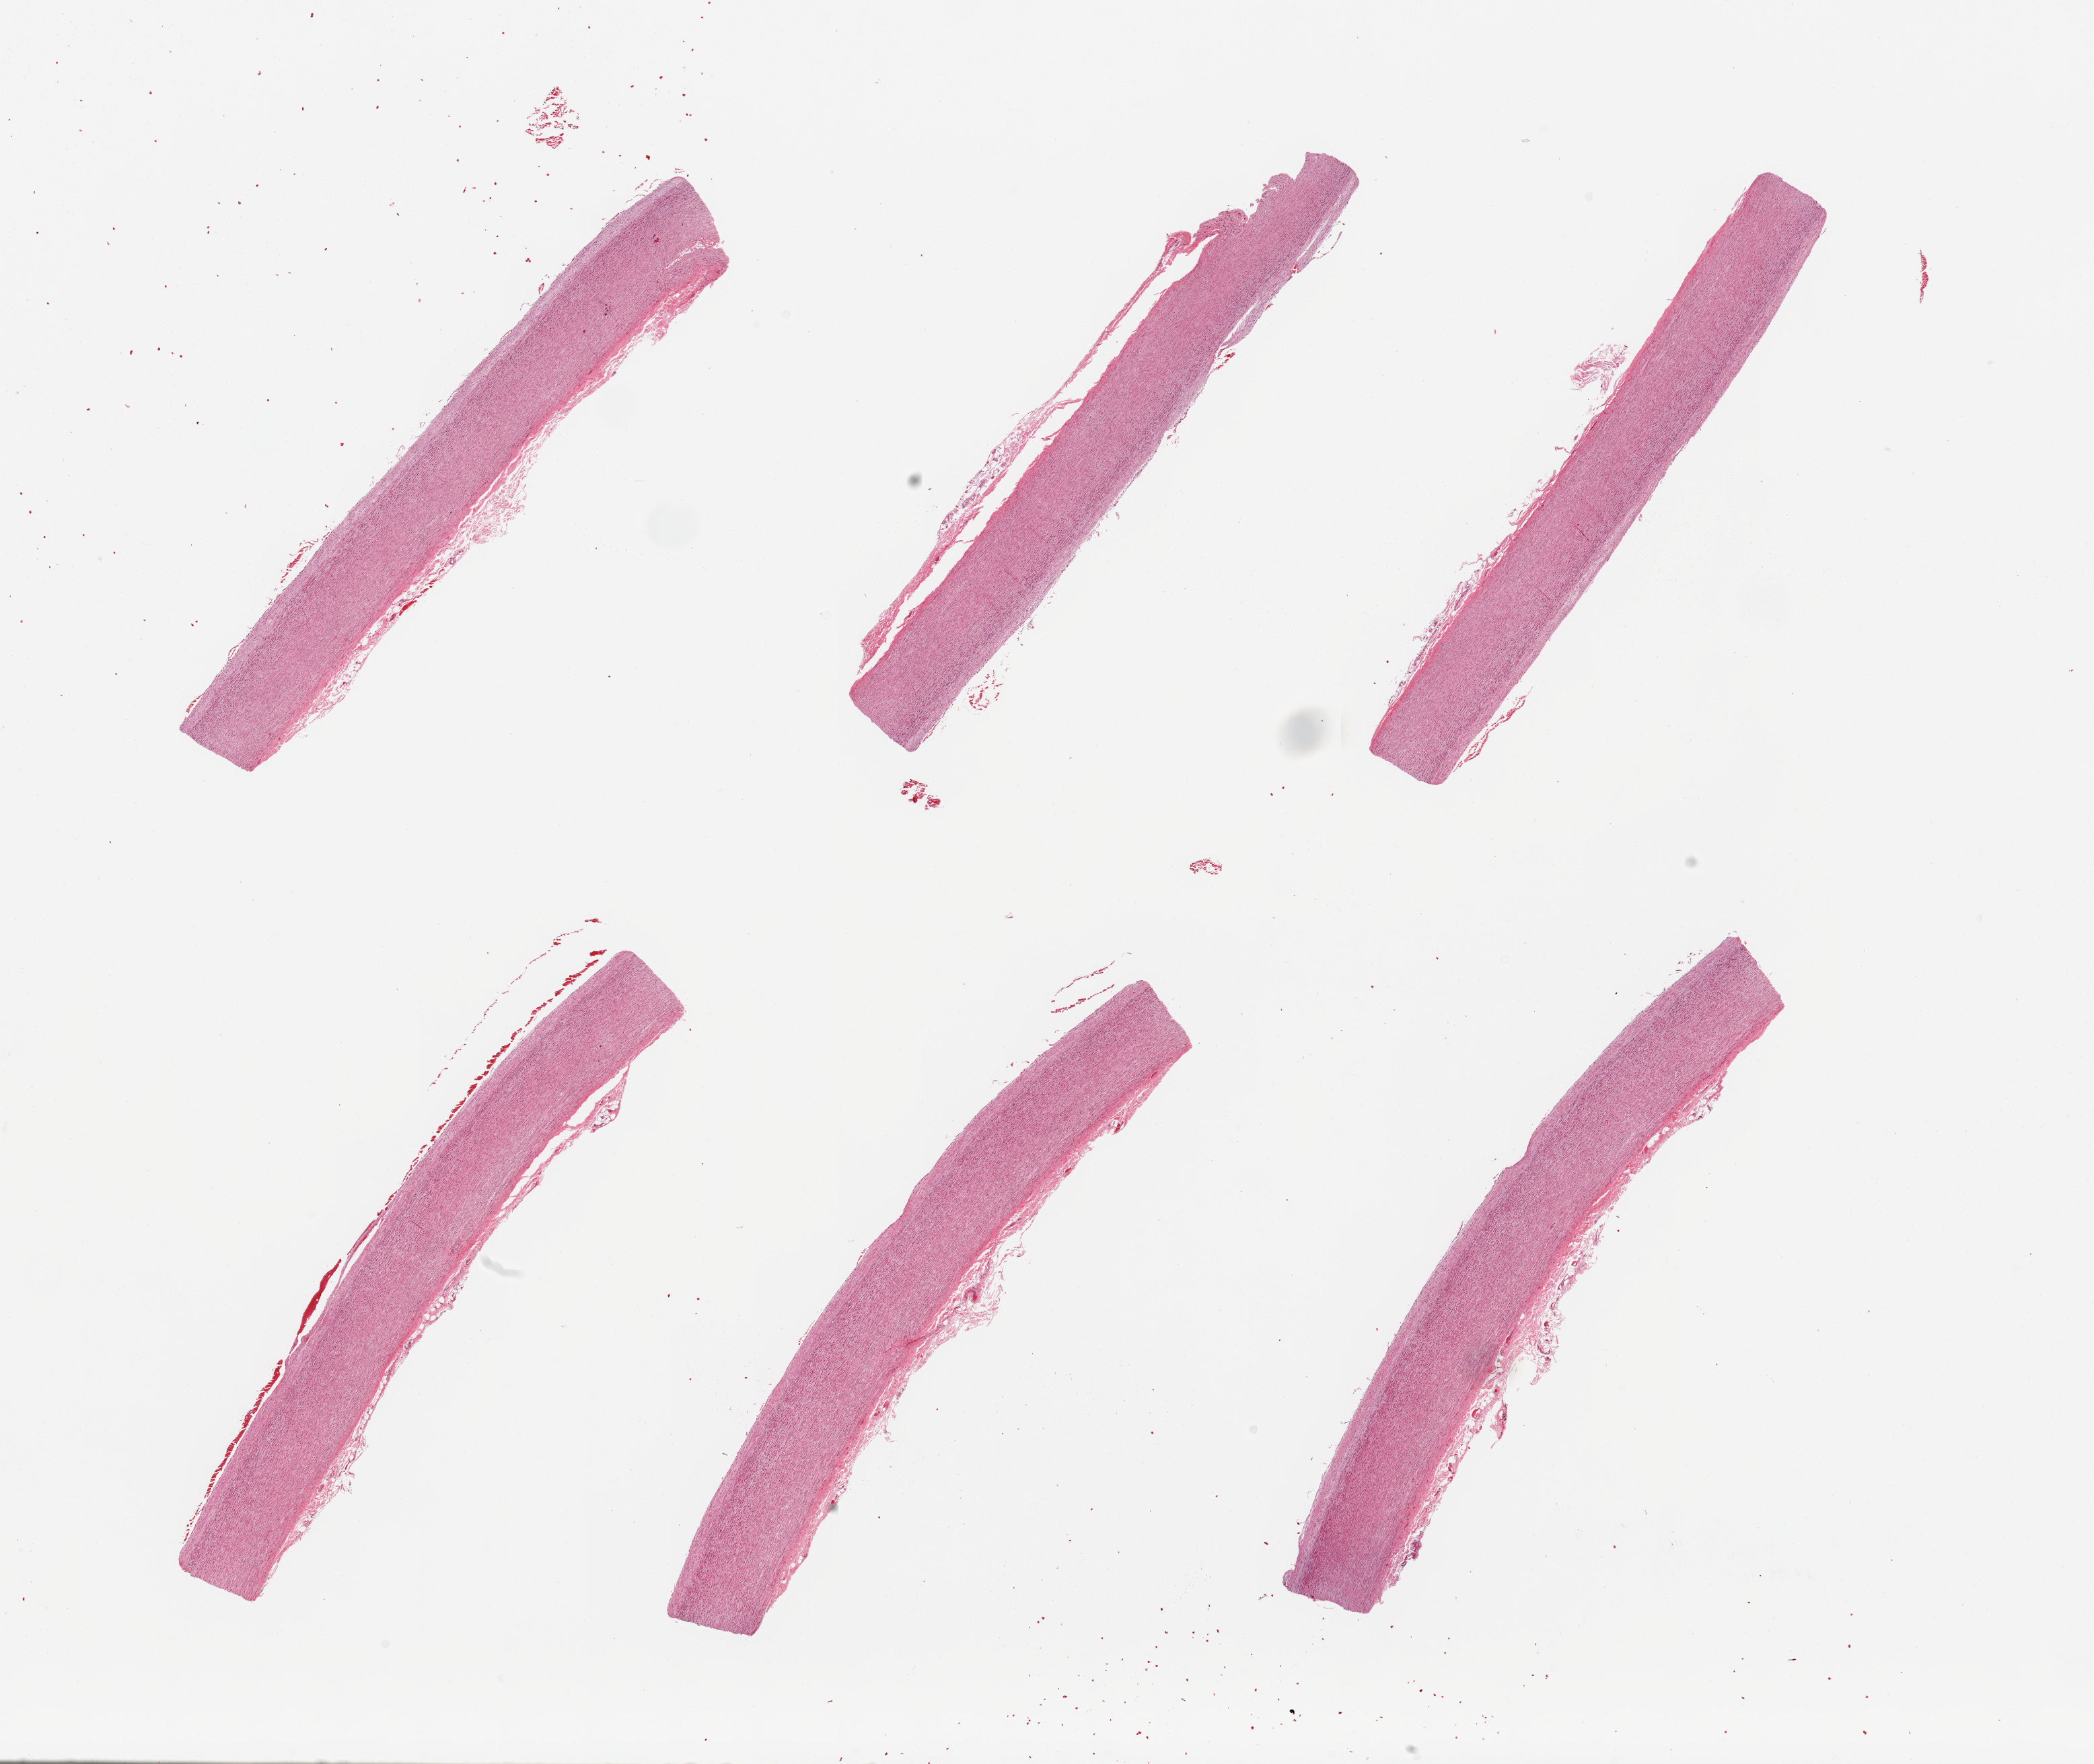
Digitized hematoxylin and eosin (H&E)-stained section, brightfield, whole scanned area (about 24.6 x 20.7 mm) shown as a low-resolution overview. PAXgene-fixed paraffin-embedded (PFPE) section. Section of aorta (target tissue). Donor tissue sample.
Review note (as recorded): 6 pieces, well trimmed.